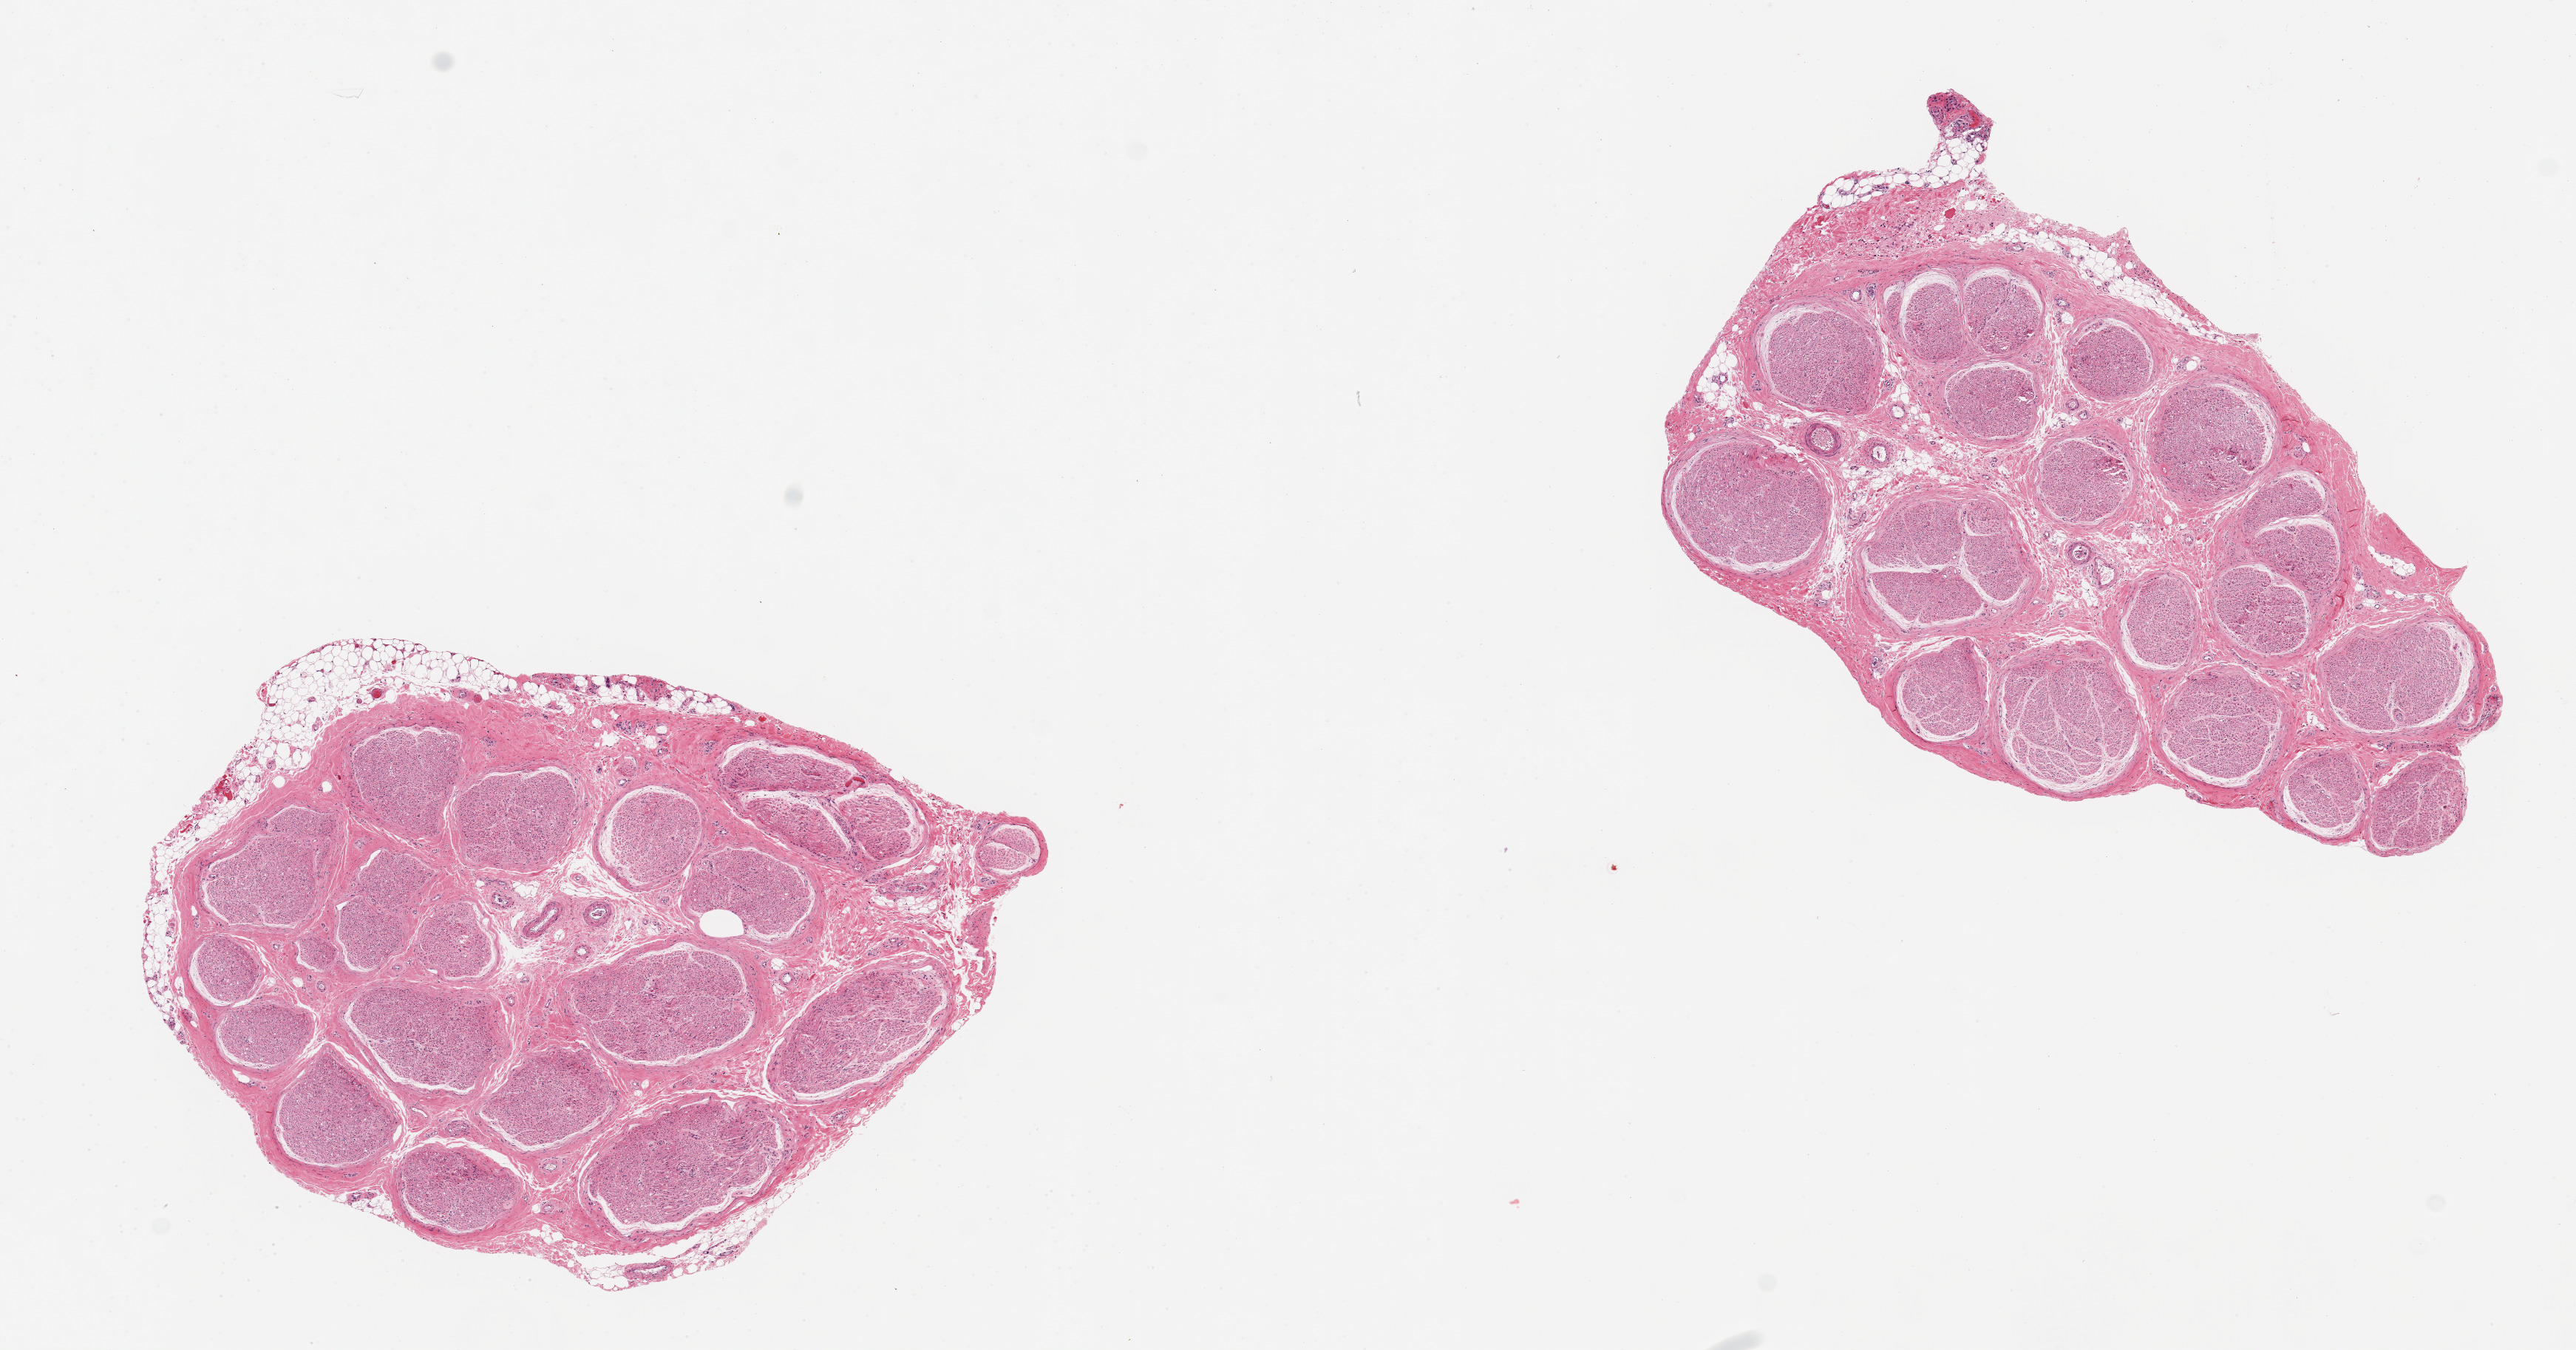
Digitized haematoxylin and eosin-stained section, brightfield, shown as a low-resolution overview of the whole scanned area (about 13.8 x 7.2 mm, slide scanned at 20x). PAXgene-fixed, paraffin-embedded tissue. Section of tibial nerve (target tissue). Donor tissue sample. Donor sex: female.
Review note (as recorded): 2 ~5x3mm aliquots; good clean specimens.